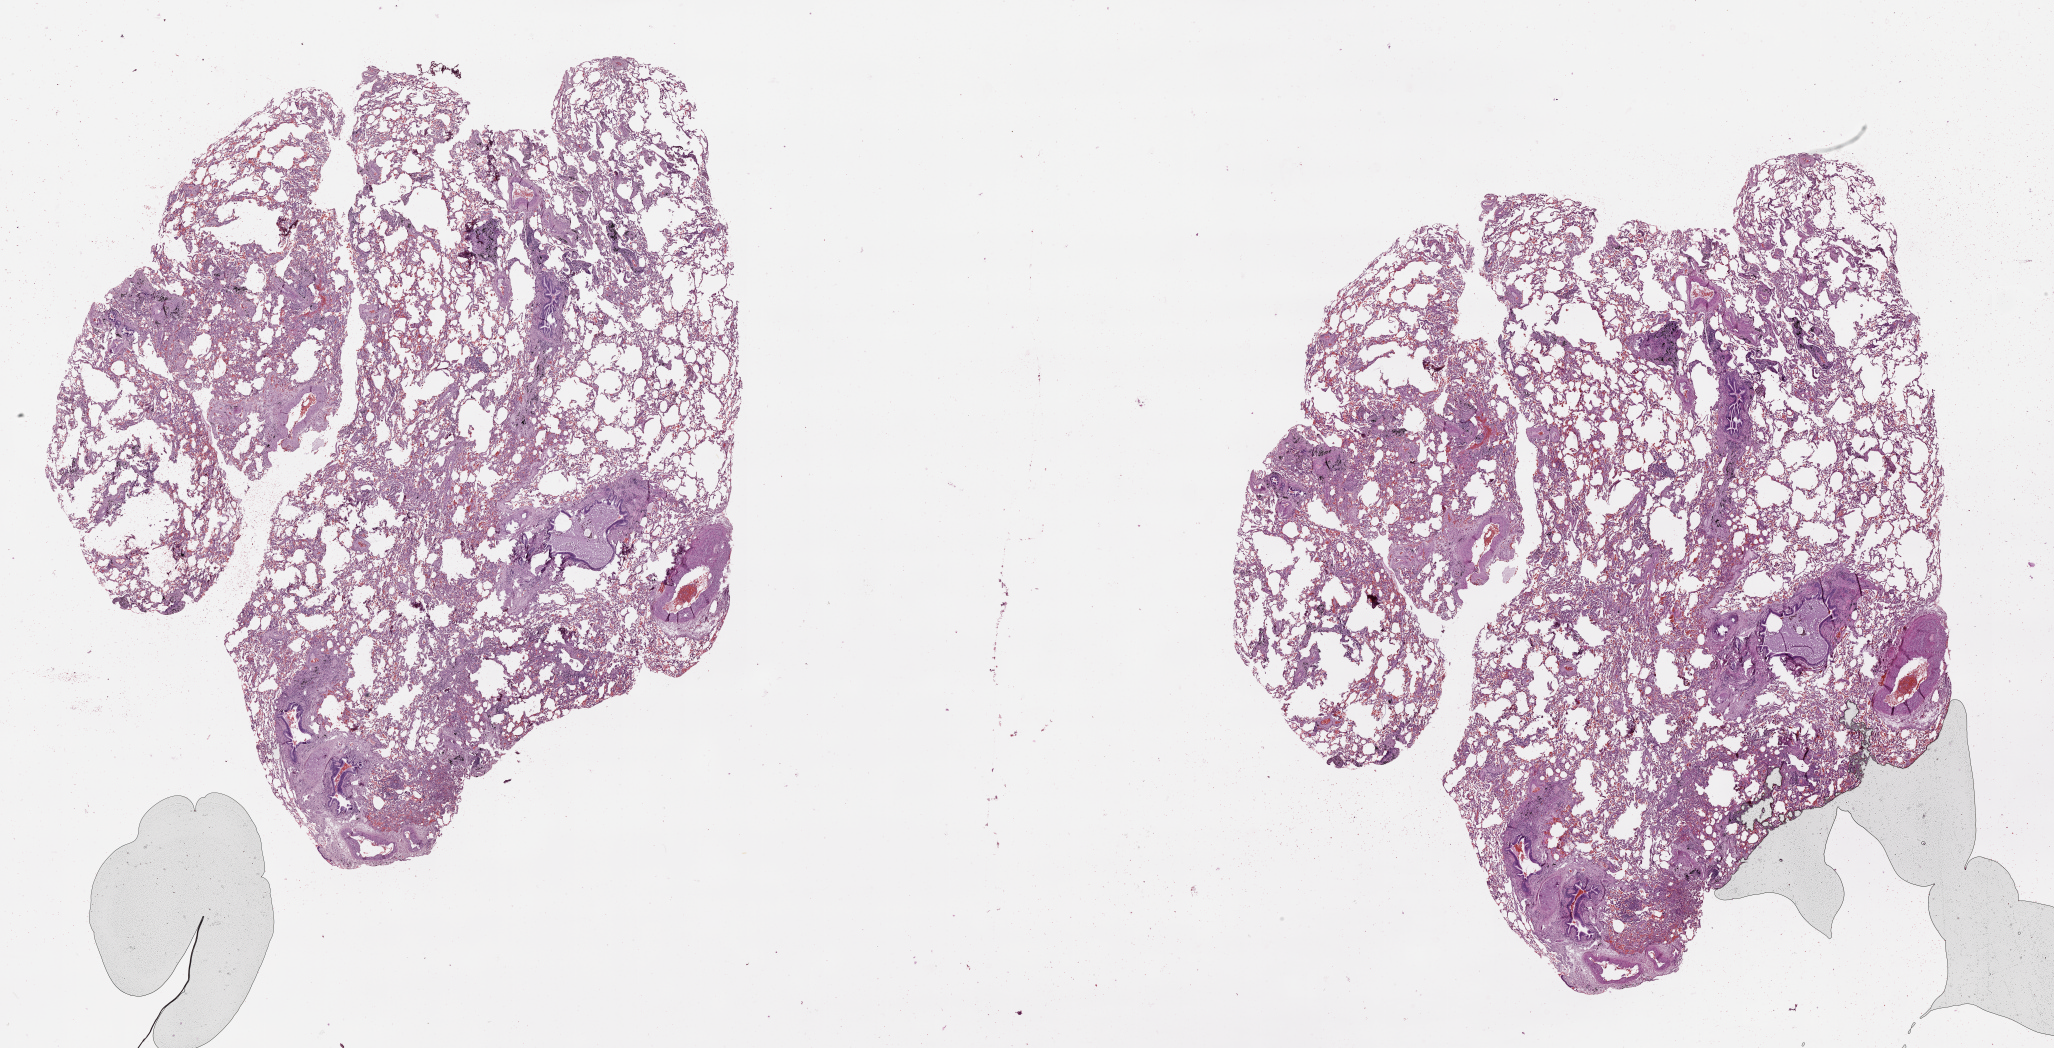
Digitized H&E tissue section (whole slide) — a low-resolution overview of the entire scanned area, about 33.1 x 16.9 mm; normal (non-tumour) tissue sample, lung. 63-year-old female patient.
This section: normal (non-tumour) tissue from the same patient. Patient diagnosis (cohort enrolment): squamous cell carcinoma (lung).